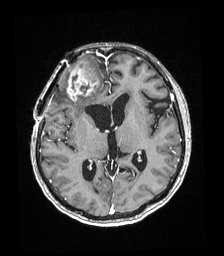
Brain MRI from a brain-tumour surgery series, one axial slice; slice 97 of 192 in the series (ordered by position); T1-weighted post-contrast; 224 × 256 image matrix, field of view 219 × 250 mm. From the clinical record (not read from this slice): histopathology: Astrocytoma; WHO grade: 4; IDH mutation: yes; tumour location: Right superficial frontal.
Structures marked on this image (manually delineated by an expert):
- tumour: bounding box [x1, y1, x2, y2] px = [67, 59, 99, 101]